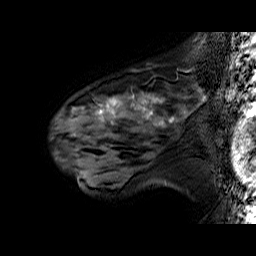
Breast MRI (dynamic contrast-enhanced), one sagittal slice. Position 42 of 60 along the scan axis. Dynamic contrast-enhanced series, time point 2 of 6 at this slice position (early post-contrast). 1.5 T. TE 6.4 ms, TR 32.9 ms. 4 mm slice thickness. 256 × 256 image matrix. Female patient. From the clinical record (not read from this slice): setting: breast cancer imaged before/during neoadjuvant chemotherapy; receptor status: HER2-positive.
Annotated regions visible in this slice (semi-automatically segmented with operator editing):
- analysis volume of interest (the breast-tissue region the enhancement analysis was run in; not a lesion): bounding box <51,81,196,160> (left, top, right, bottom; pixels)
- tumour enhancement mask (voxels above the 100 % enhancement threshold inside the analysis volume of interest): <96,93,172,121>